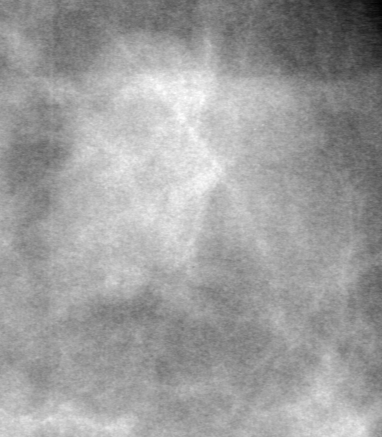
Region of interest cut from a scanned film mammogram (one marked finding); left breast; CC view; BI-RADS breast density category 1 (scale 1–4).
Mass, shape lobulated, margins obscured; BI-RADS assessment category 0; pathology result (as recorded, not read from the image): benign.